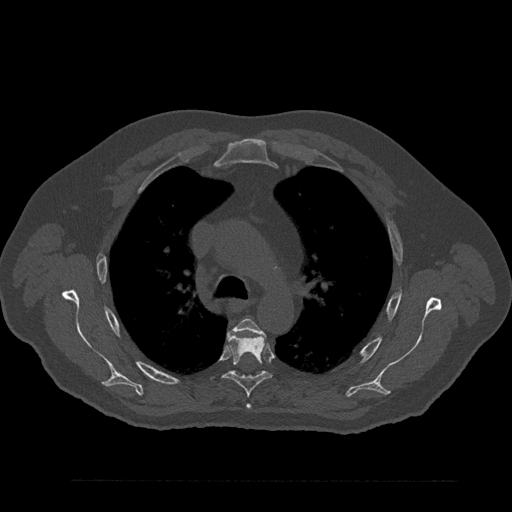
CT including the spine, one axial slice; slice 606 of 797 in the series (ordered by position); reconstruction kernel Br40s/3; 120 kVp; bone window (W 1800 / L 400 HU); 0.5 mm slice thickness; 512 × 512 image matrix. Male patient, age 61 years. From the clinical record (not read from this slice): primary cancer: prostate.
Outlined on this slice (semi-automatic segmentation, software-assisted and operator-edited):
- T4 vertebra: bounding box <235,319,265,410> (left, top, right, bottom; pixels)
- T5 vertebra: <223,333,272,397>
- T6 vertebra: <258,373,263,376>